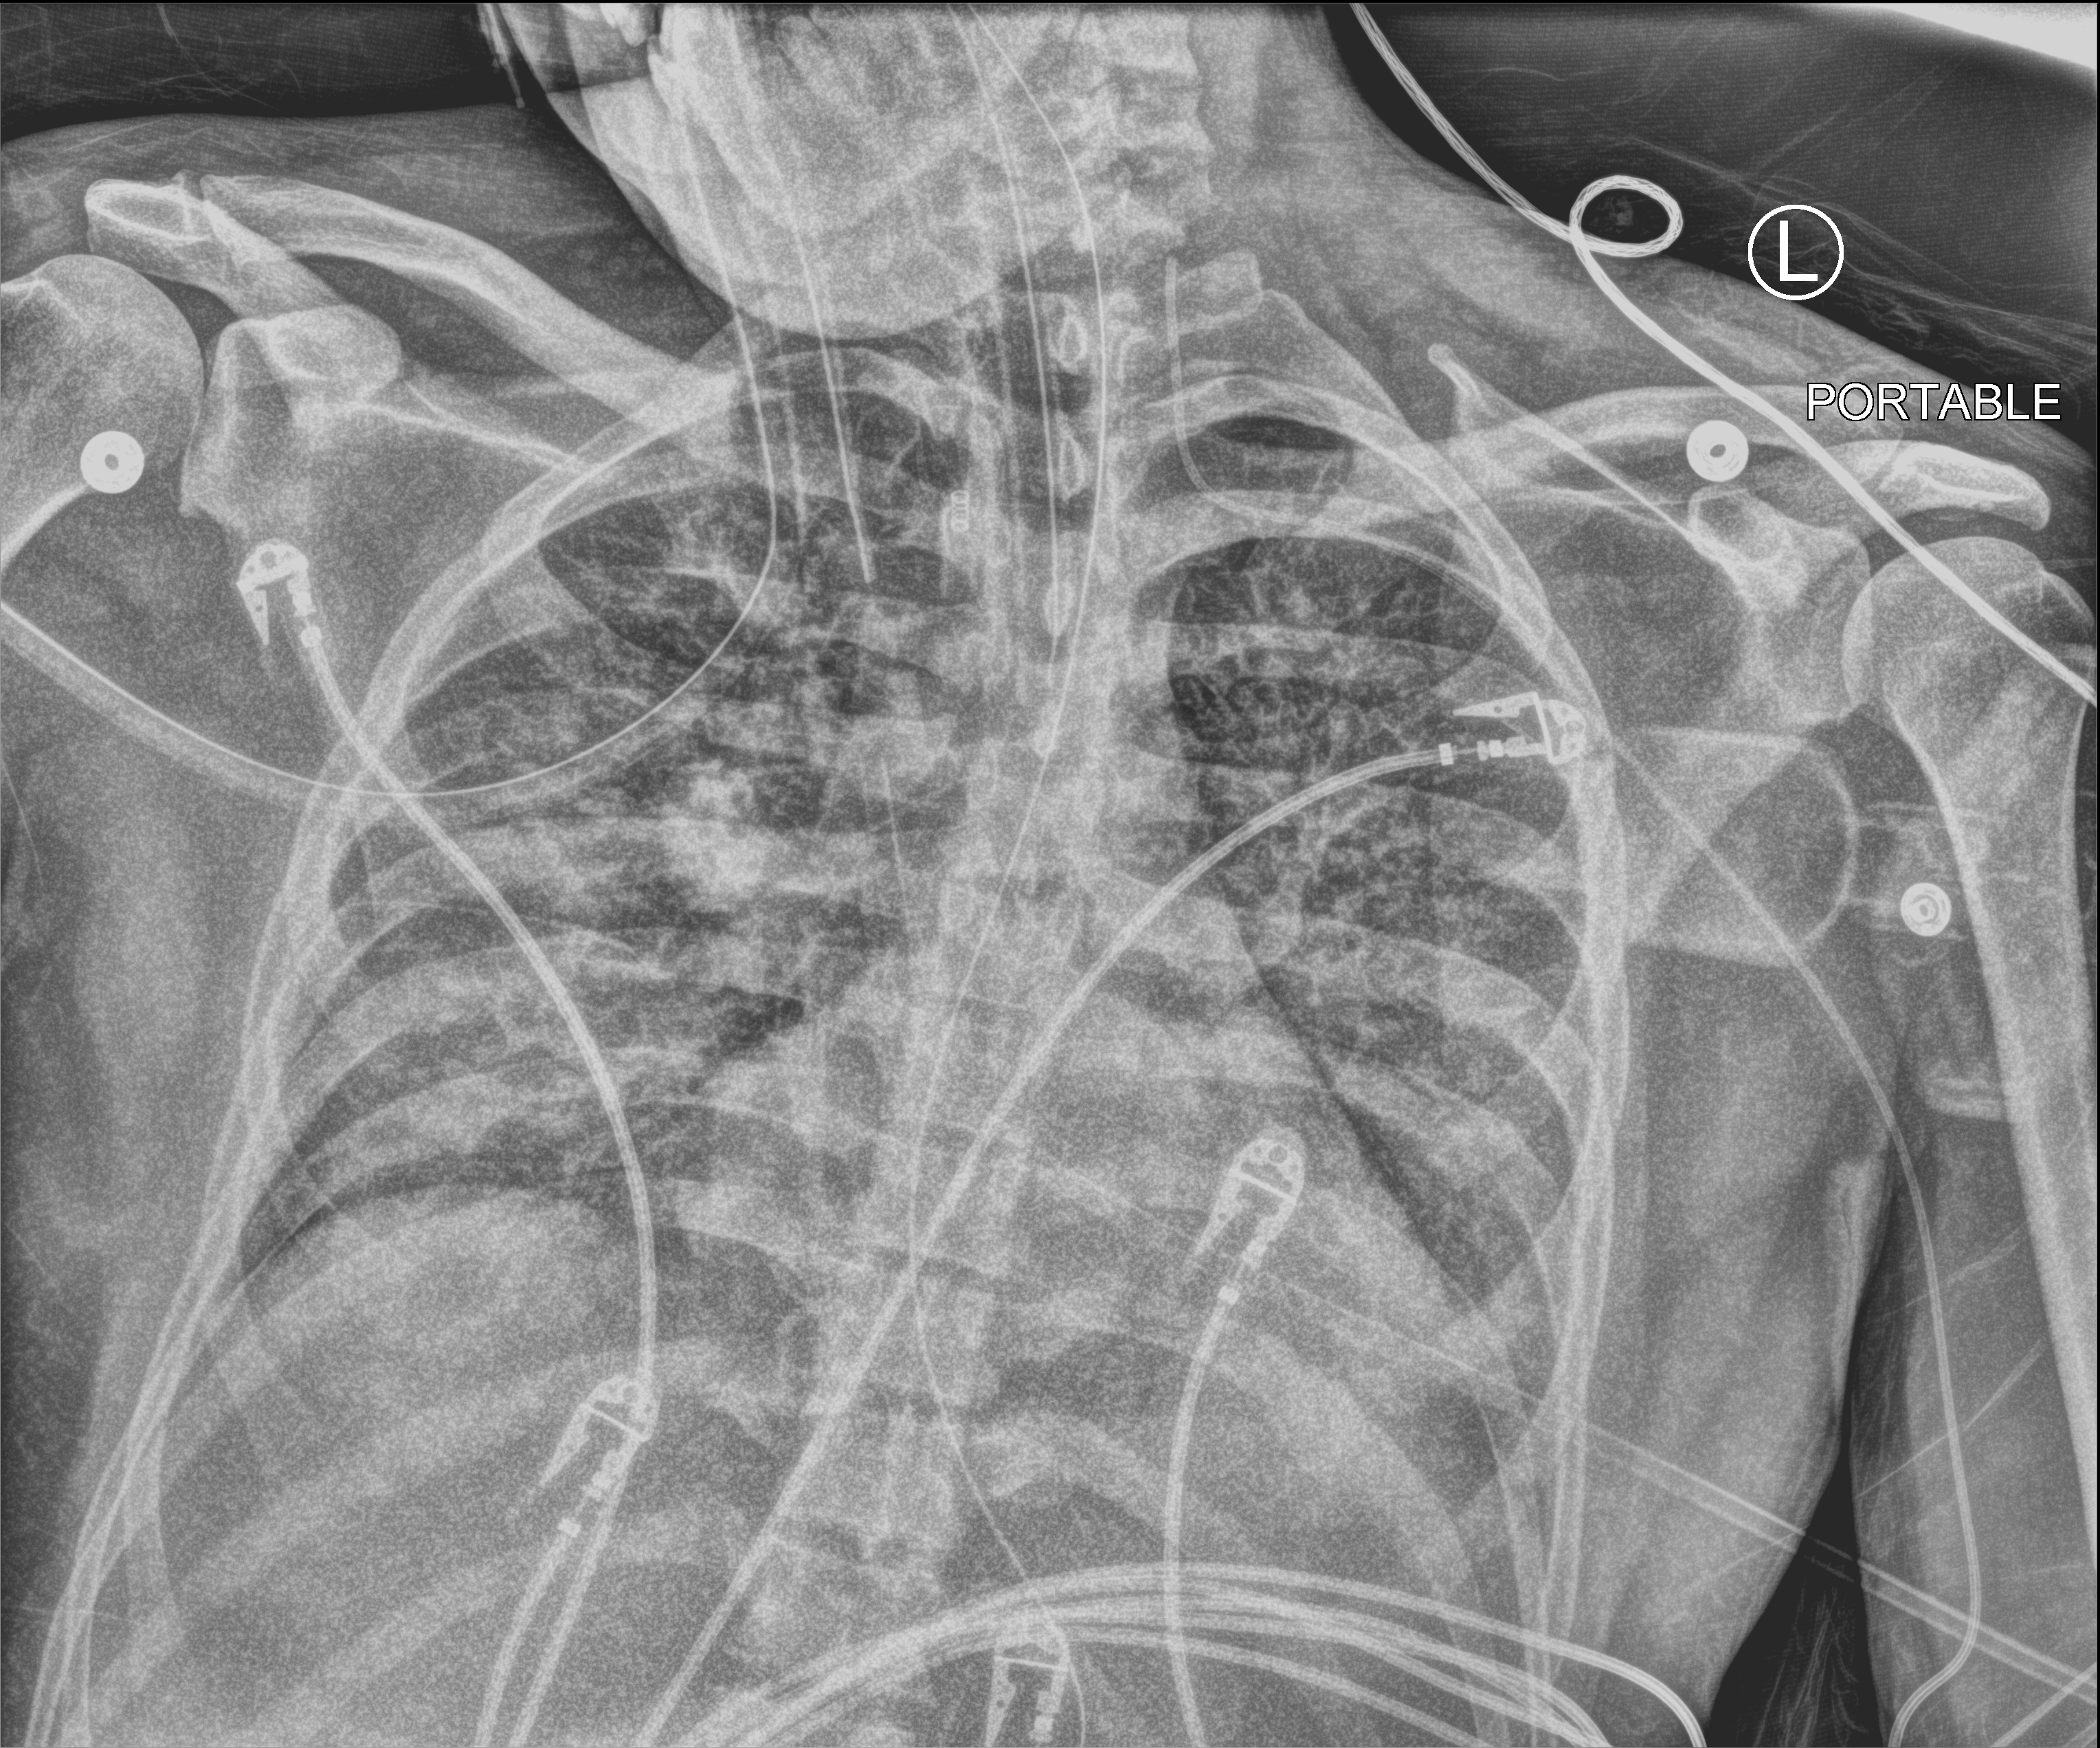
Bedside chest radiograph (computed radiography). Patient hospitalised with COVID-19; male, aged 18–59 years.
Admission-level facts for this patient (not findings on this image; timing relative to this image not recorded): diabetes (admission record): no; mechanically ventilated during this hospital stay: yes.